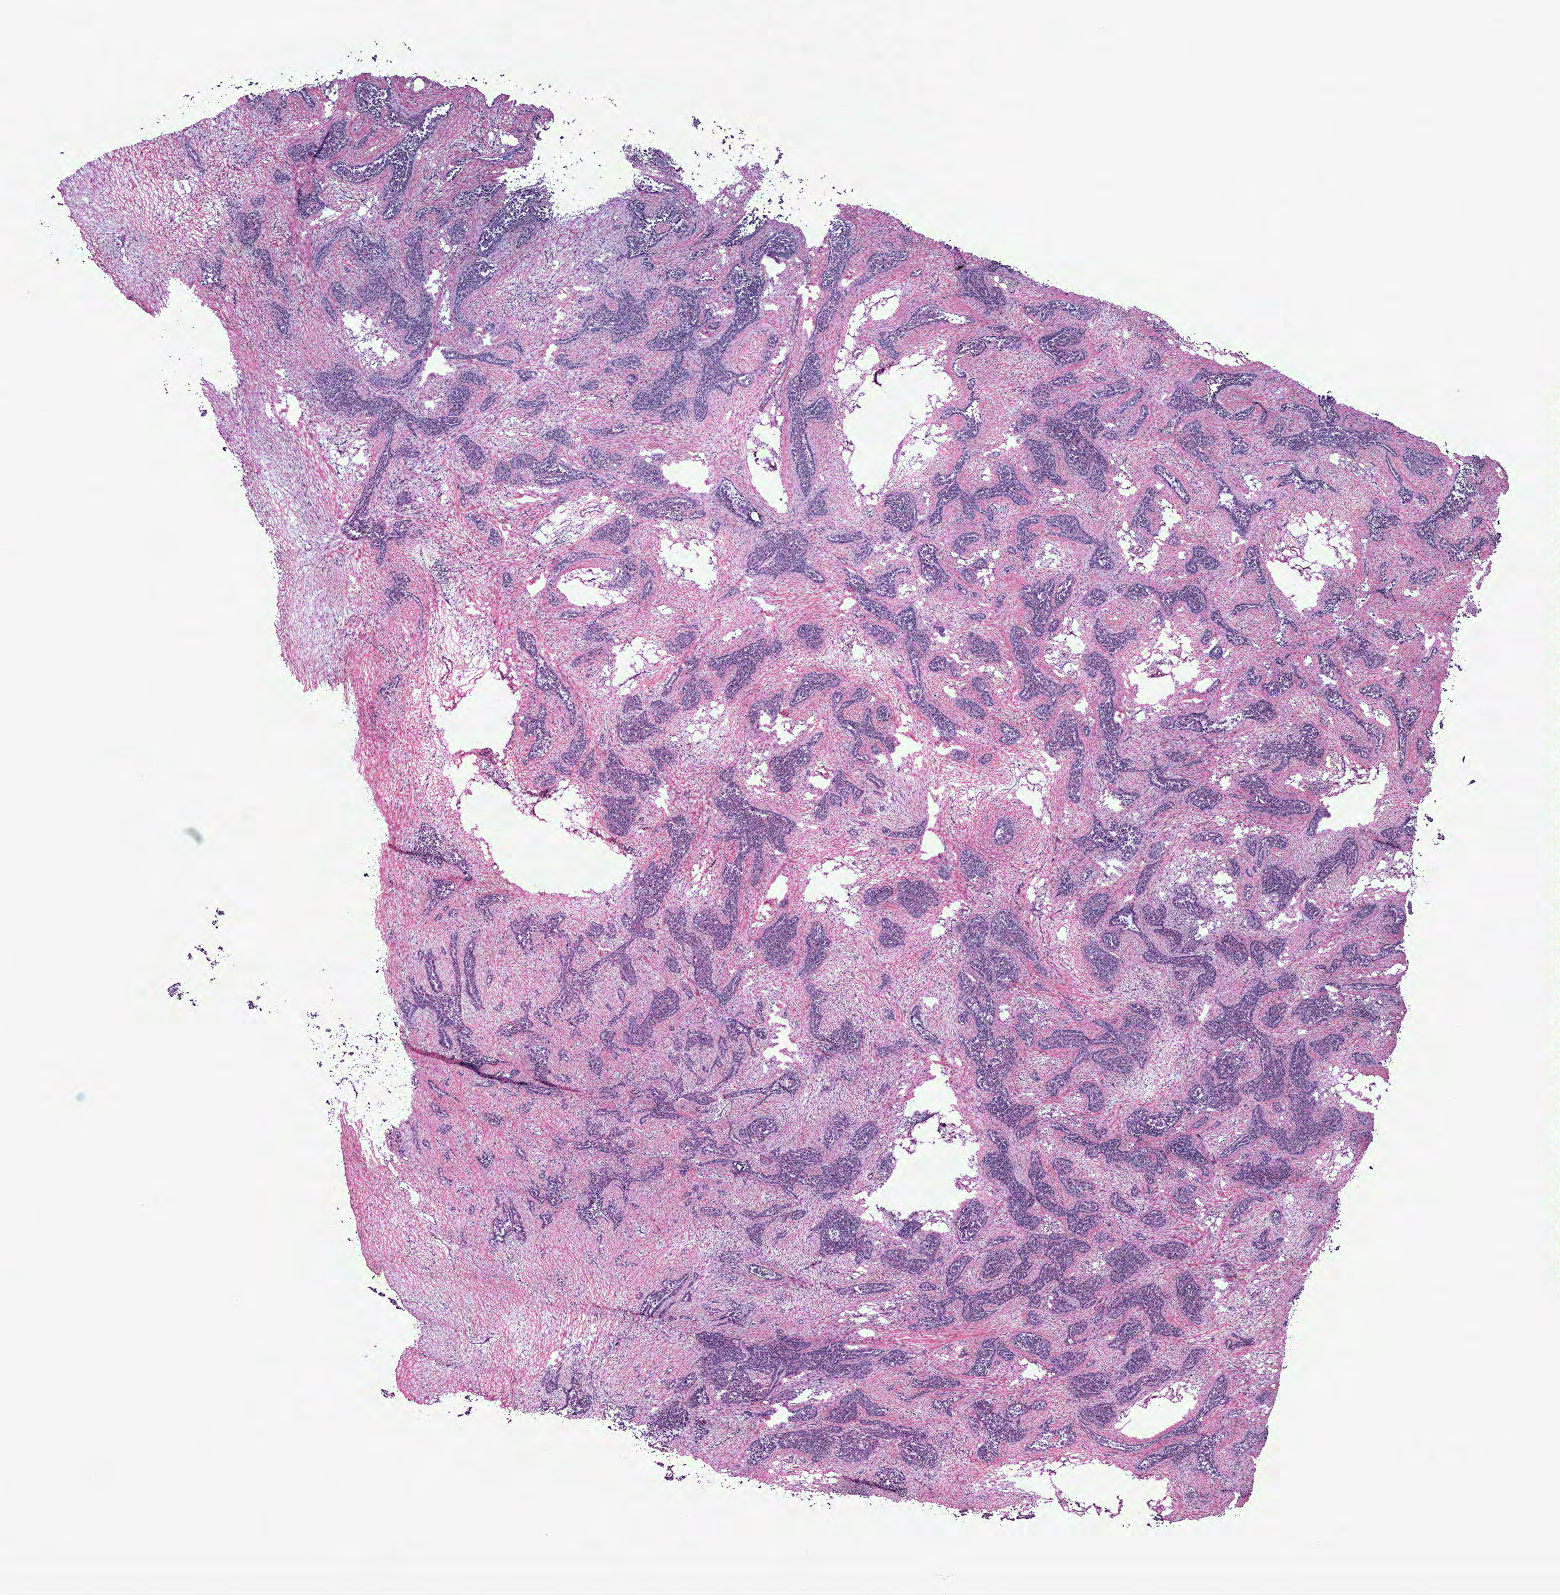
Whole-slide histology image, H&E, whole scanned area (about 12.5 x 12.8 mm, slide scanned at 40x) shown as a low-resolution overview, tumour tissue sample, ovary. Female, 57 y/o.
- primary tumour site (as recorded): ovary
- diagnosis: Serous adenocarcinoma, NOS